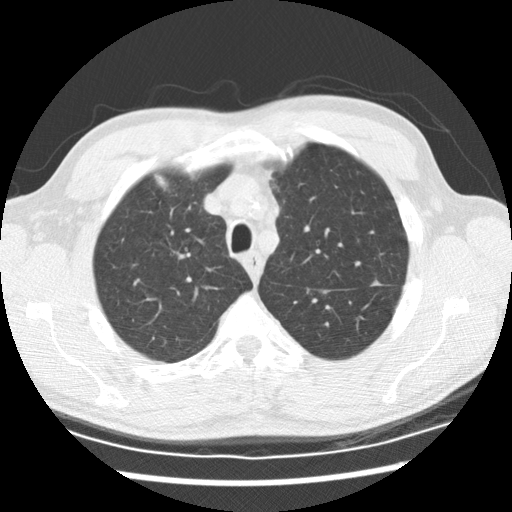
Low-dose screening chest CT, one axial slice; position 164 of 208 along the scan axis; 120 kVp; lung window (W 1500 / L -600 HU); 2.5 mm slice thickness; 512 × 512 image matrix, field of view 340 × 340 mm.
Outlined on this slice (manually delineated by an expert):
- lesion 3 (tumor, upper lobe of left lung): bounding box [x1, y1, x2, y2] px = [371, 279, 382, 286]